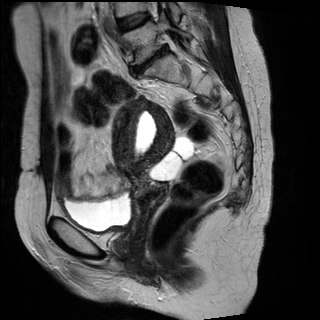
Pelvic MRI for cervical cancer, one sagittal slice; slice 13 of 29 in the series (ordered by position); T2-weighted; 1.5 T; TE 89 ms, TR 2930 ms; 320 × 320 image matrix, field of view 260 × 260 mm. Patient: female, 45 years.
Annotated regions visible in this slice (manually delineated by an expert):
- uterus and cervix: bounding box <113,99,176,216> (left, top, right, bottom; pixels)